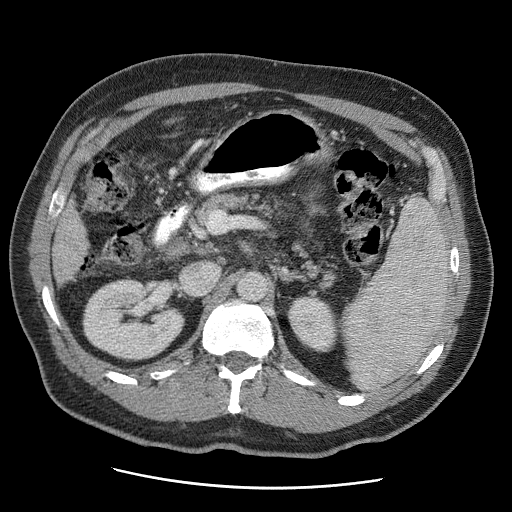
Contrast-enhanced abdominal CT (liver protocol), one axial slice; reconstruction kernel STANDARD; 120 kVp; soft-tissue window (W 400 / L 40 HU); 2.5 mm slice thickness; 512 × 512 image matrix. Case-level facts recorded for this patient, not image findings: diagnosis: hepatocellular carcinoma (patient treated with transarterial chemoembolisation; whether this scan precedes or follows treatment is not stated here); TNM stage (as recorded): Stage-IIIA; Child-Pugh class: A; tumour differentiation: moderately differentiated; tumour nodularity: multinodular.
Structures marked on this image (semi-automatic segmentation, software-assisted and operator-edited):
- liver parenchyma outside the tumour (the mass and vessels are separate outlines, so this box may not span the whole liver): bounding box (x1, y1, x2, y2) in pixels: (52, 204, 88, 284)